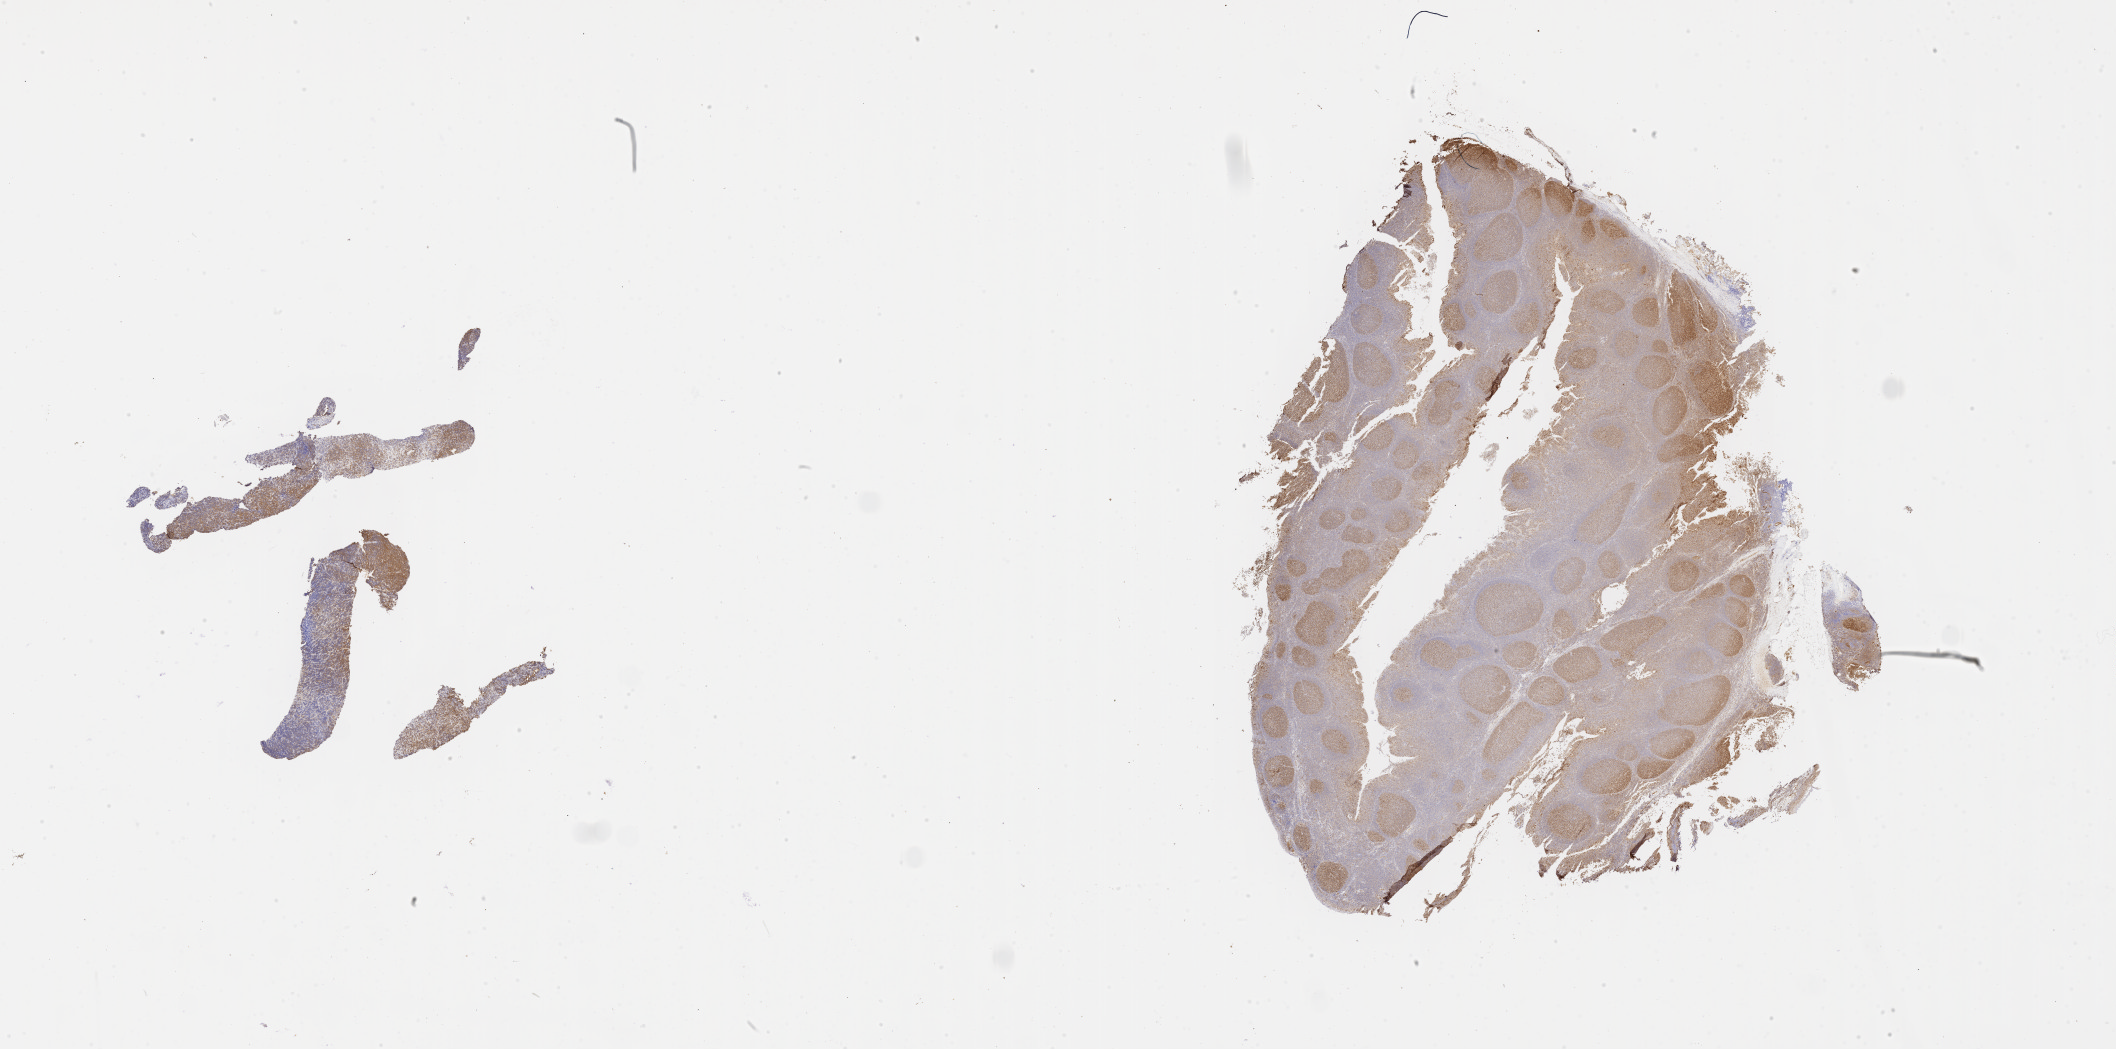
Whole-slide image, immunohistochemical stain for BCL6 — low-resolution overview of the scanned area, about 34.2 x 17.0 mm, tumor tissue, site: abdomen proper. Male patient; age at initial diagnosis 2 years.
* diagnosis: Diffuse large B-cell lymphoma, NOS